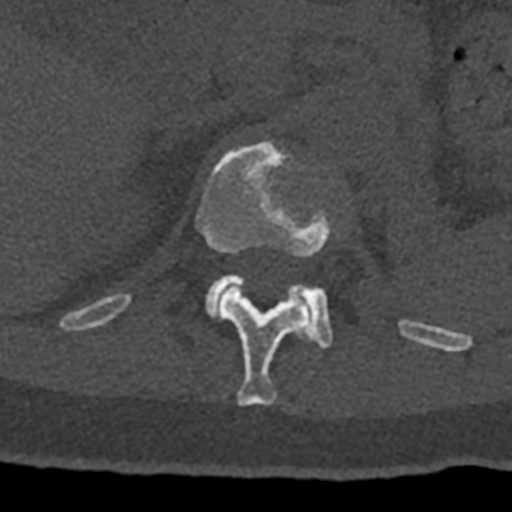
CT including the spine, one axial slice; slice 474 of 797 in the series (ordered by position); reconstruction kernel Br40s/3; bone window (W 1800 / L 400 HU); 0.5 mm slice thickness; 512 × 512 image matrix, field of view 160 × 160 mm. Patient: male, 74 years. From the clinical record (not read from this slice): primary cancer: renal; vertebrae with lytic lesions (as recorded): T10, L1, L2, L3, L4, L5.
Outlined on this slice (semi-automatically segmented with operator editing):
- L1 vertebra: bounding box [x1, y1, x2, y2] px = [205, 274, 333, 349]
- T12 vertebra: [70, 141, 432, 405]